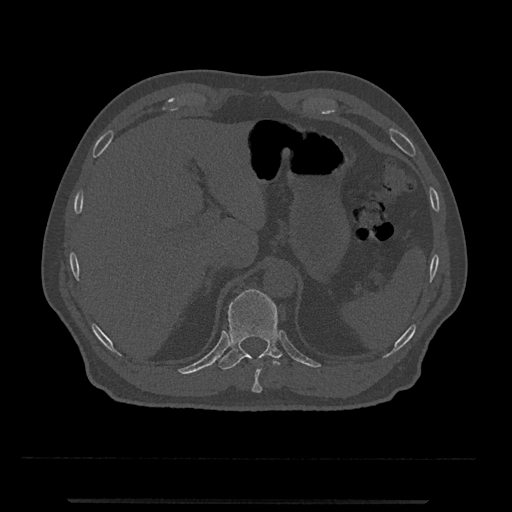
CT including the spine, one axial slice; 120 kVp; bone window (W 1800 / L 400 HU); 512 × 512 image matrix, field of view 419 × 419 mm. Patient: male, 63 years. Case-level facts recorded for this patient, not image findings: primary cancer: prostate.
Outlined on this slice (semi-automatic segmentation, software-assisted and operator-edited):
- T10 vertebra: bounding box <252,355,276,393> (left, top, right, bottom; pixels)
- T11 vertebra: <218,289,283,370>